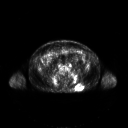
FDG PET of an extremity soft-tissue mass (from a PET/CT study), one axial slice; position 94 of 267 along the scan axis; 128 × 128 image matrix. Male patient, age 61 years. Case-level facts recorded for this patient, not image findings: histological type: pleiomorphic leiomyosarcoma; grade: high; site of the primary tumour: left buttock.
Annotated regions visible in this slice (expert contour drawn on MRI and transferred to this co-registered scan by the dataset authors):
- gross tumour volume including surrounding oedema: bounding box [x1, y1, x2, y2] px = [76, 85, 83, 91]
- gross tumour volume (mass): [76, 85, 83, 91]